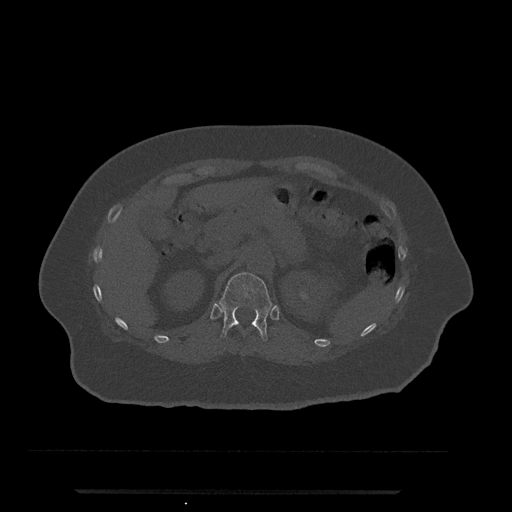
CT including the spine, one axial slice; position 181 of 797 along the scan axis; 120 kVp; bone window (W 1800 / L 400 HU); 0.5 mm slice thickness; 512 × 512 image matrix, field of view 440 × 440 mm. Patient: female, 51 years. From the clinical record (not read from this slice): primary cancer: neuro; vertebrae with lytic lesions (as recorded): T8.
Structures marked on this image (semi-automatic segmentation, software-assisted and operator-edited):
- T12 vertebra: box from (x=219, y=273) to (x=273, y=341) px